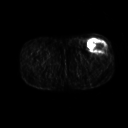
FDG PET of an extremity soft-tissue mass (from a PET/CT study), one axial slice; slice 236 of 267 in the series (ordered by position); 3.27 mm slice thickness; 128 × 128 image matrix, field of view 500 × 500 mm. Male patient, age 64 years. From the clinical record (not read from this slice): histological type: extraskeletal osteosarcoma; grade: high; site of the primary tumour: thigh.
Outlined on this slice (expert contour drawn on MRI and transferred to this co-registered scan by the dataset authors):
- gross tumour volume (mass): box from (x=87, y=39) to (x=108, y=53) px